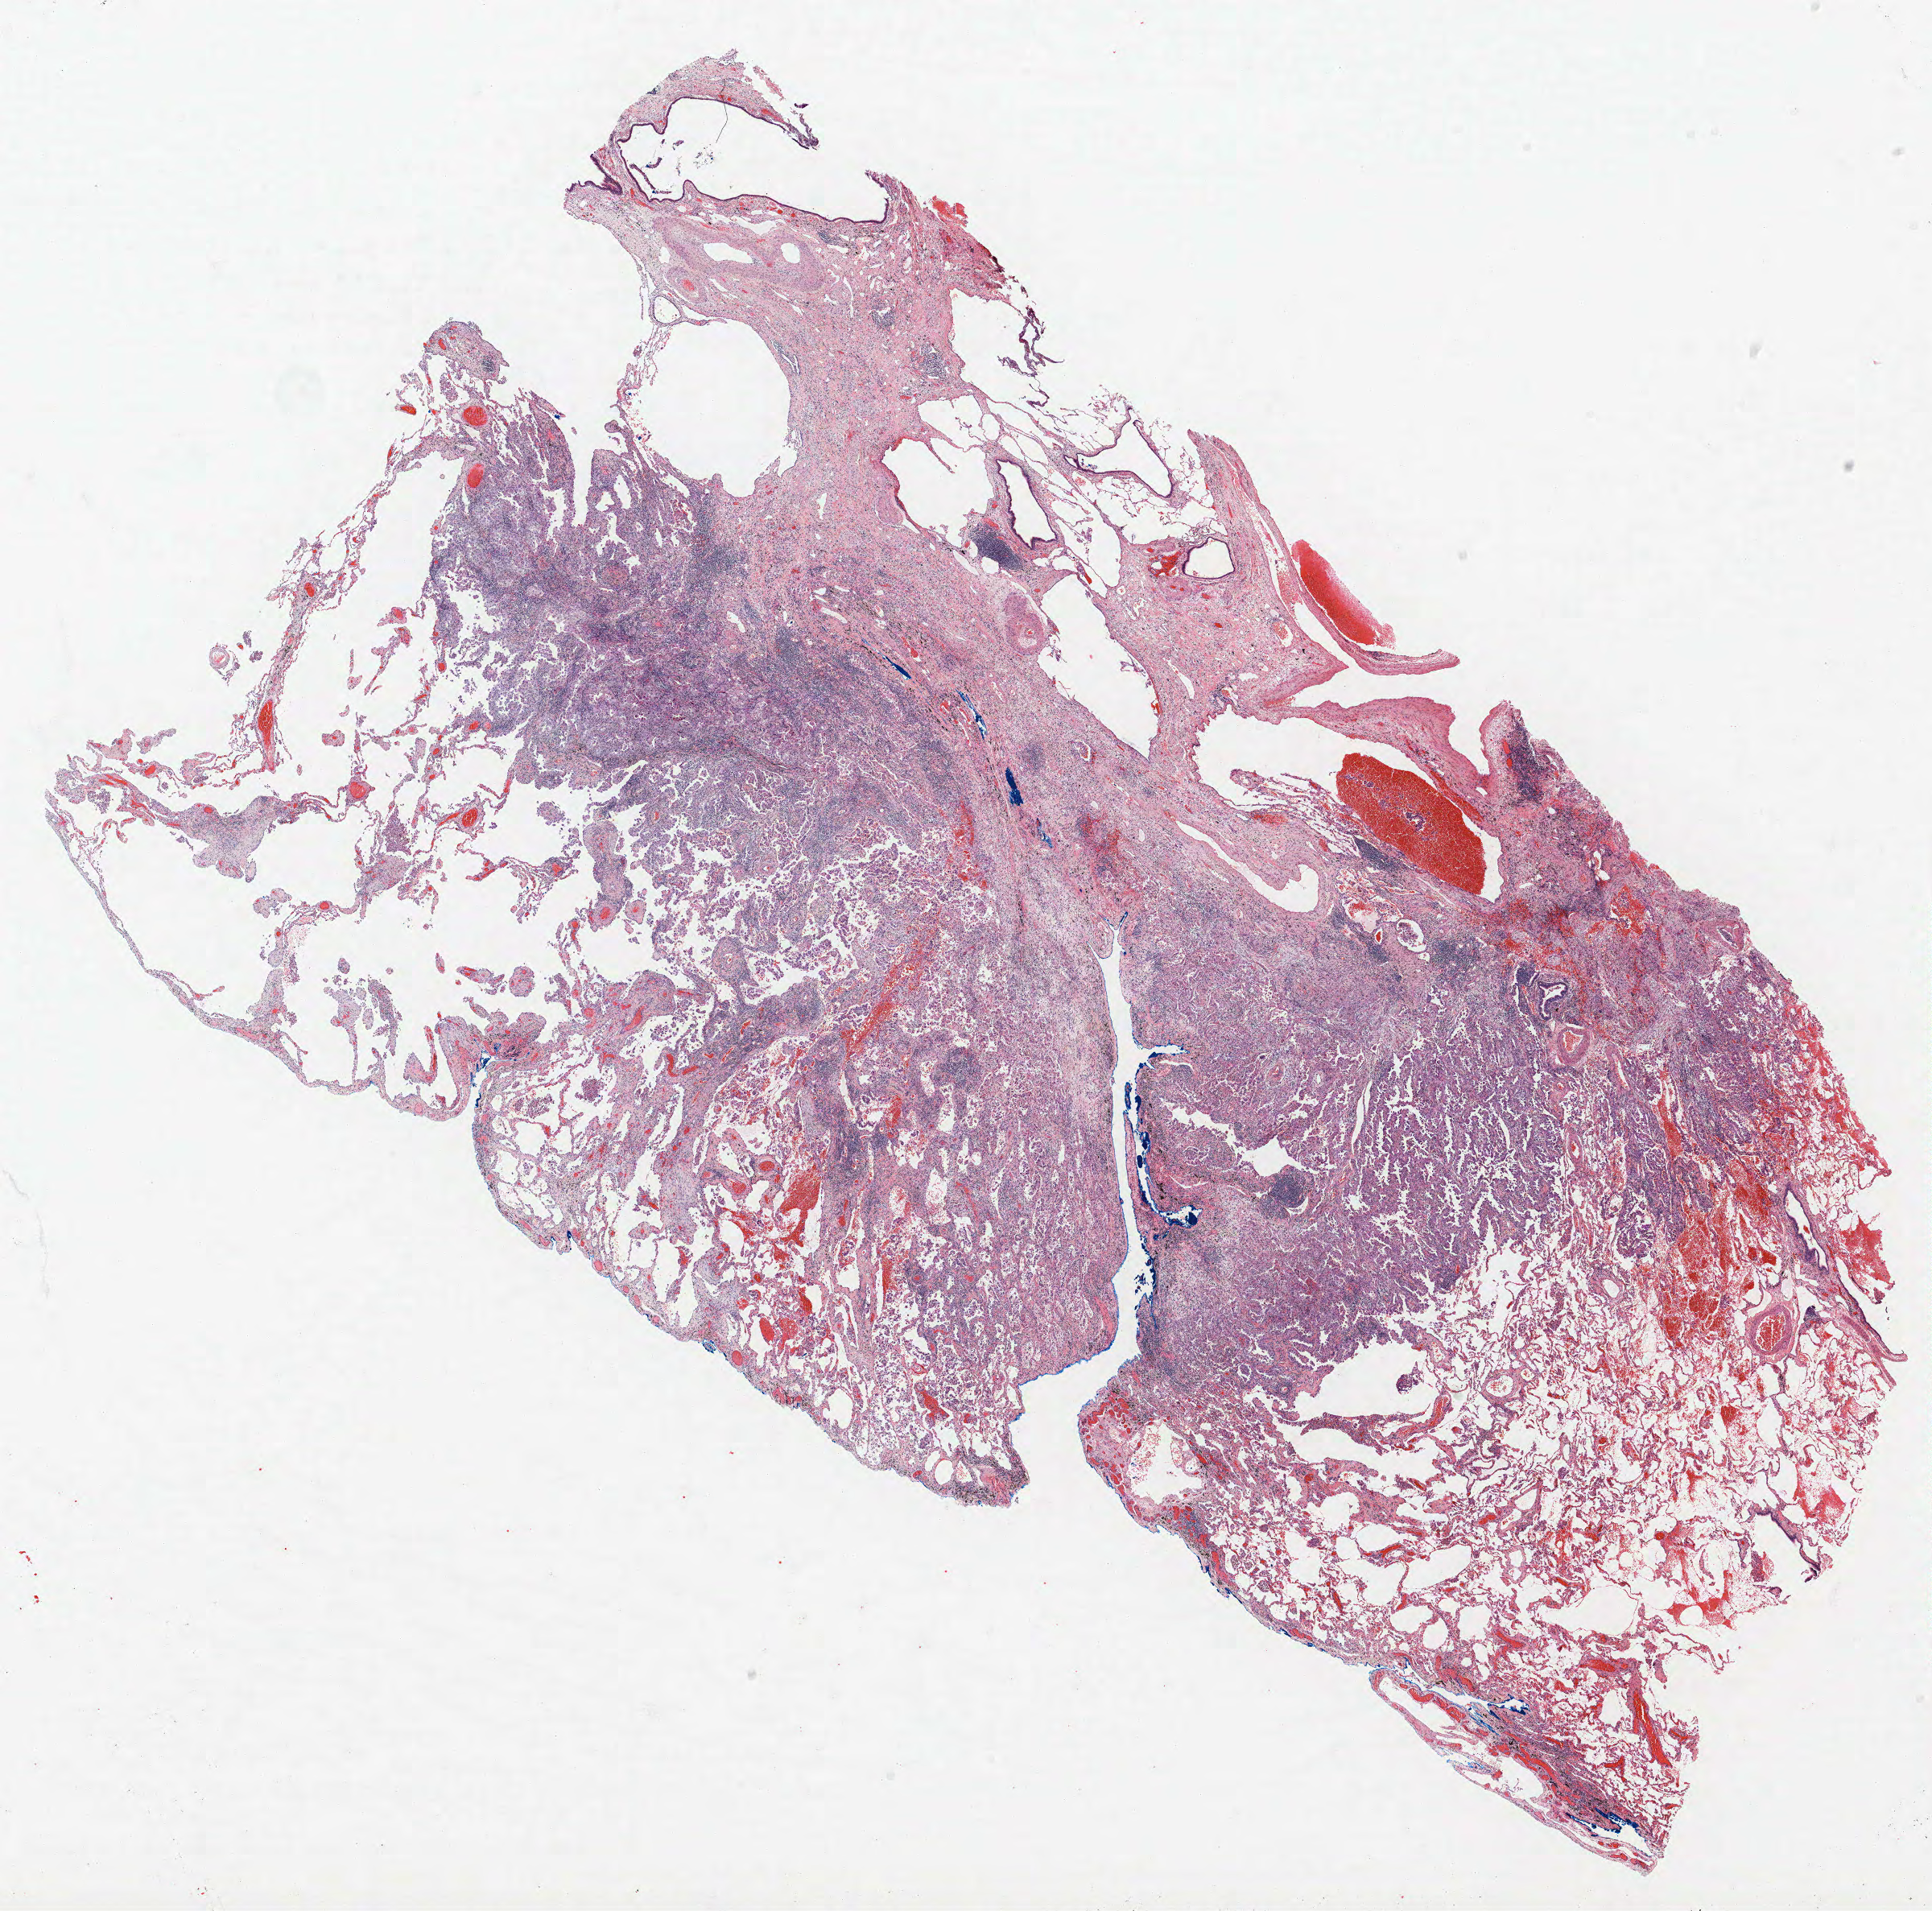
H&E-stained whole-slide image, a low-resolution overview of the entire scanned area, about 19.2 x 19.0 mm (acquisition: 40x scan), formalin-fixed paraffin-embedded (FFPE) section, lung tissue. Female, age 61 at enrolment. Current smoker at enrolment. Grade: poorly differentiated (G3).
Primary tumour location (clinical record): left lower lobe. Participant's lung-cancer diagnosis: Non-small cell carcinoma. Tumour size (pathology): 100 mm. Stage (AJCC 6th edition): IB.